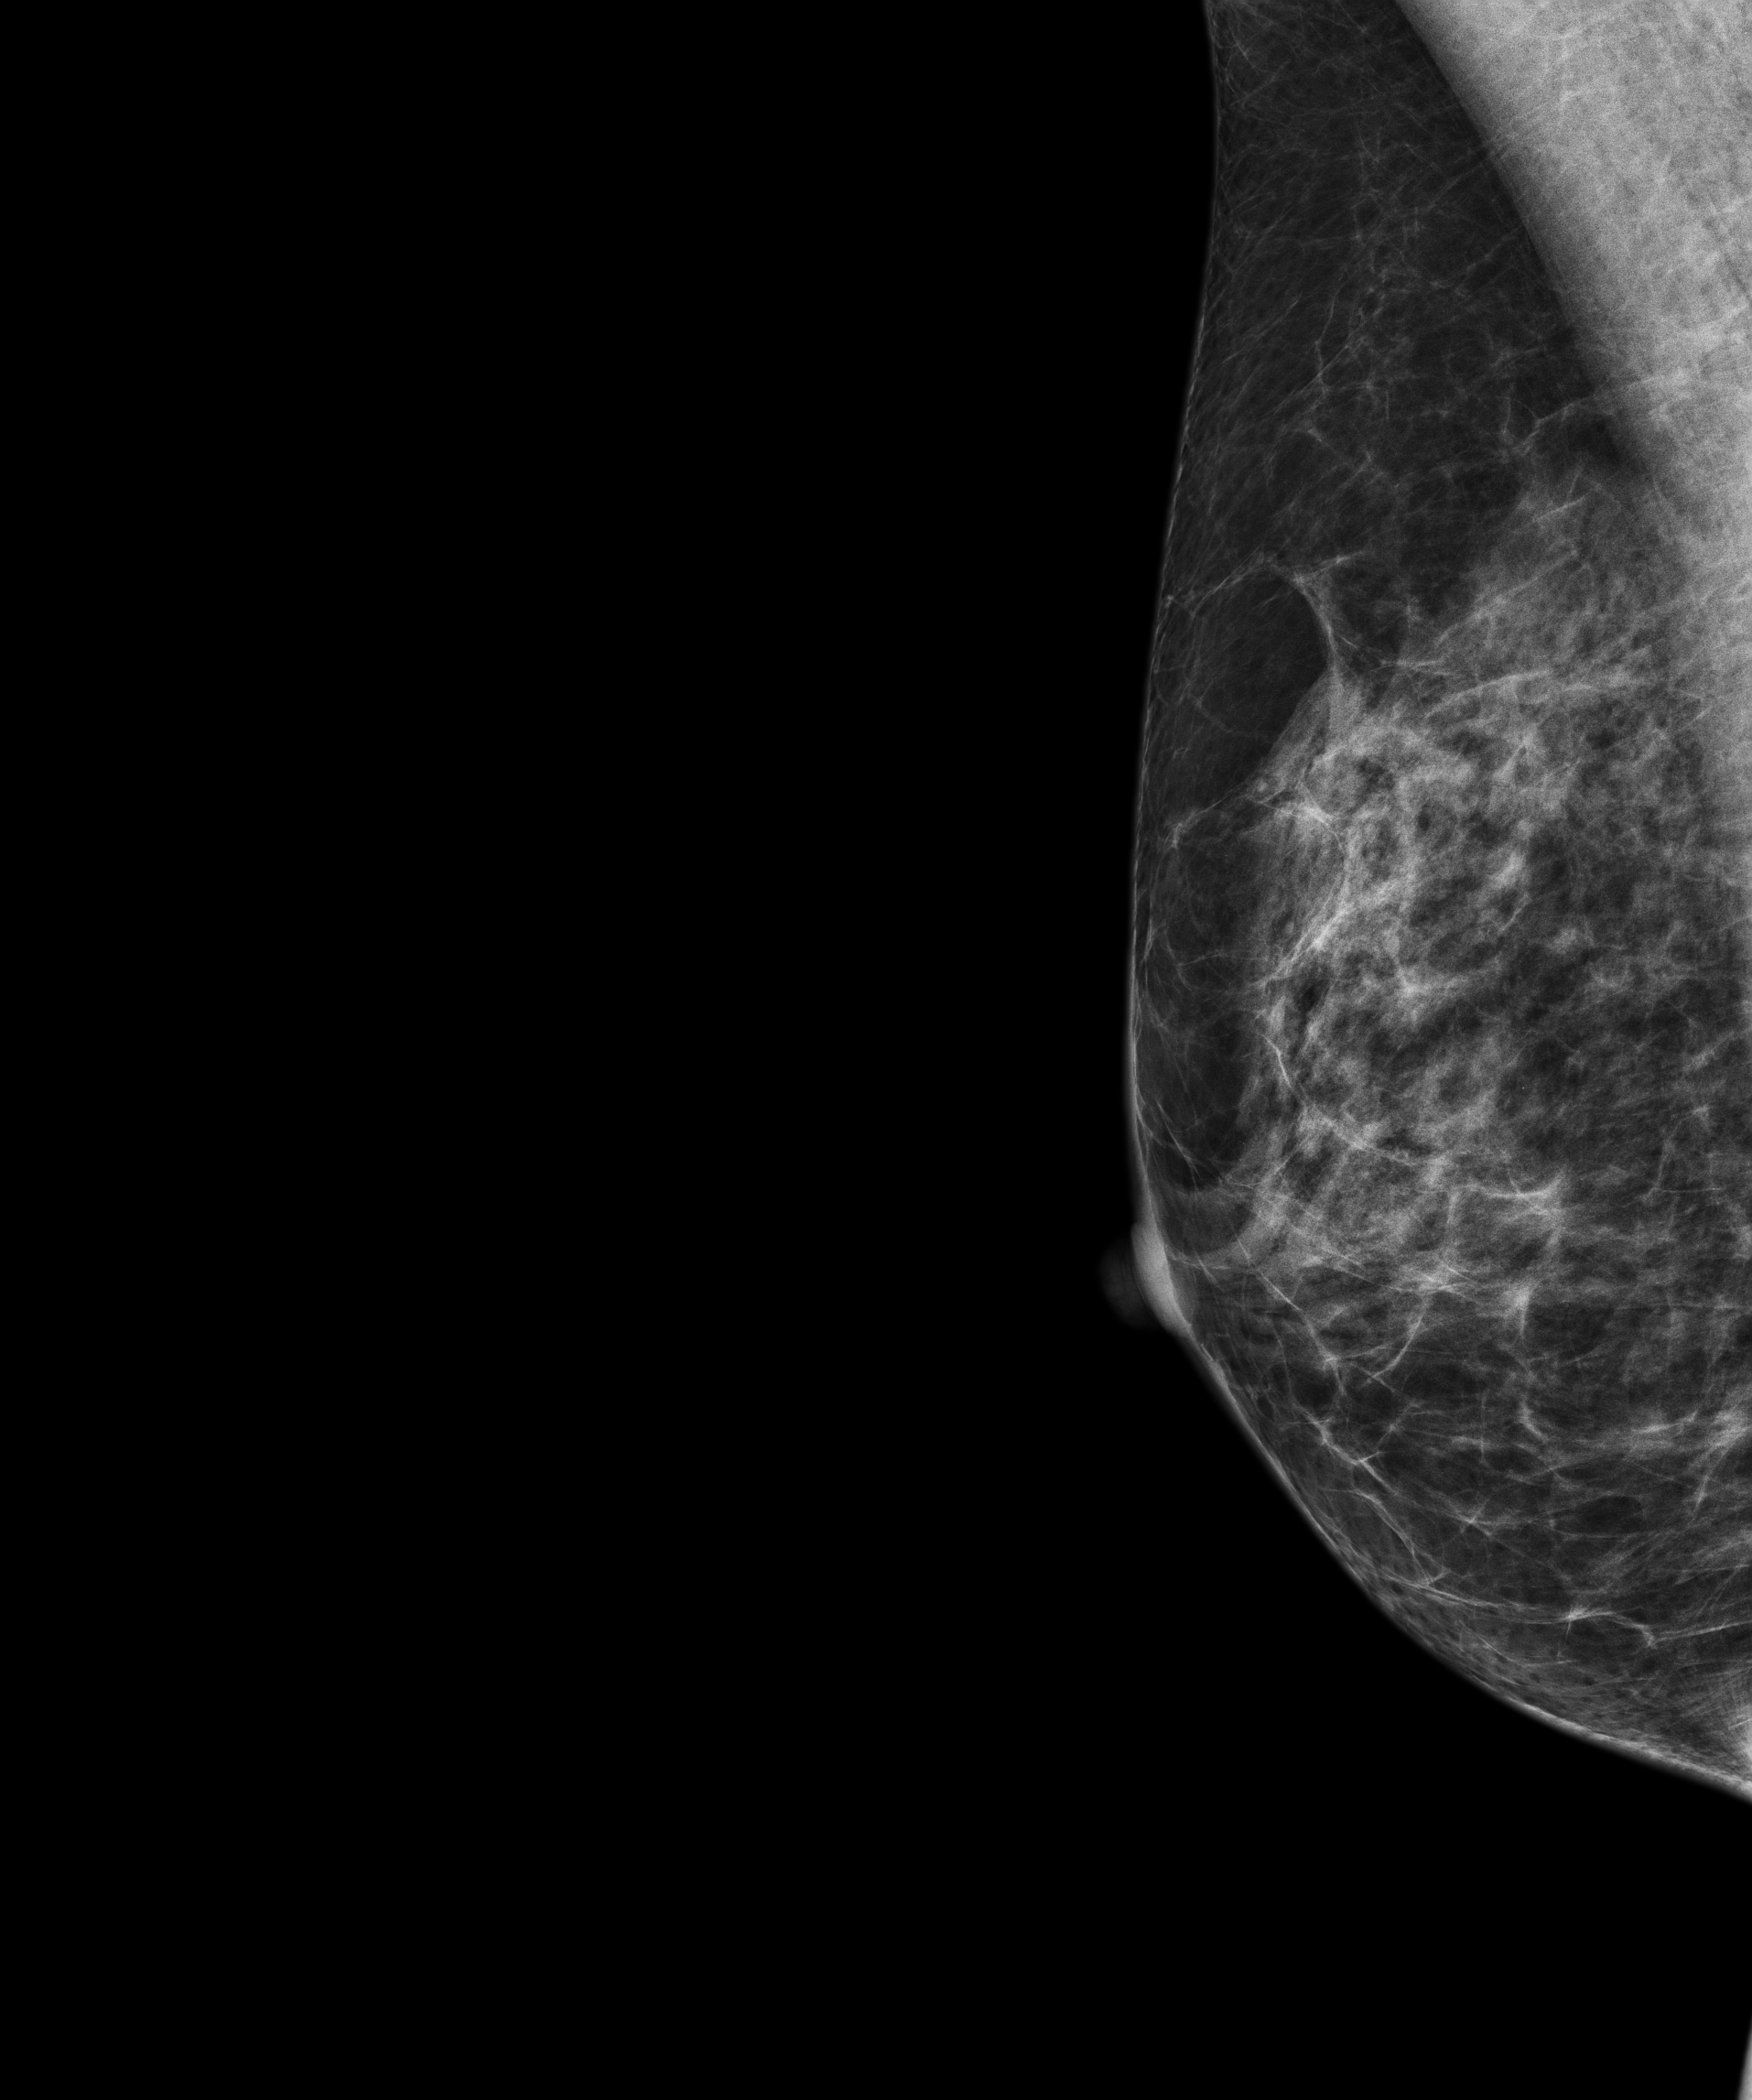
Digital mammogram (FFDM), right breast, MLO view, screening examination, compressed breast thickness 46 mm, system: Senographe Essential ADS_56.21.3. Patient: female, 61 years.
Final BI-RADS assessment for this screening round (tomosynthesis exam, both breasts): category 1.